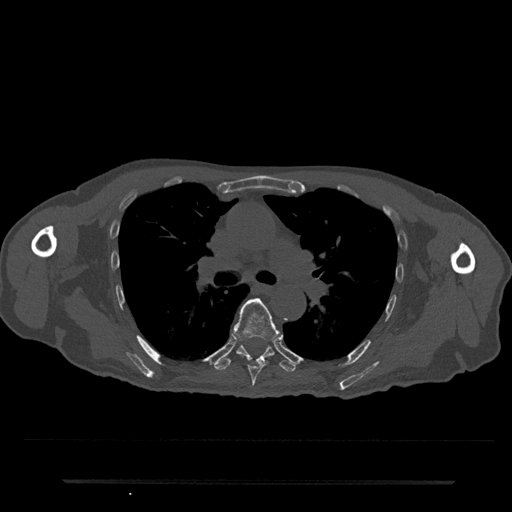
CT including the spine, one axial slice. Position 510 of 797 along the scan axis. Bone window (W 1800 / L 400 HU). 0.5 mm slice thickness. 512 × 512 image matrix, field of view 427 × 427 mm. Patient: male, 74 years. Case-level facts recorded for this patient, not image findings: primary cancer: prostate.
Annotated regions visible in this slice (semi-automatically segmented with operator editing):
- T6 vertebra: bounding box [x1, y1, x2, y2] px = [233, 298, 280, 387]
- T7 vertebra: [215, 345, 296, 372]